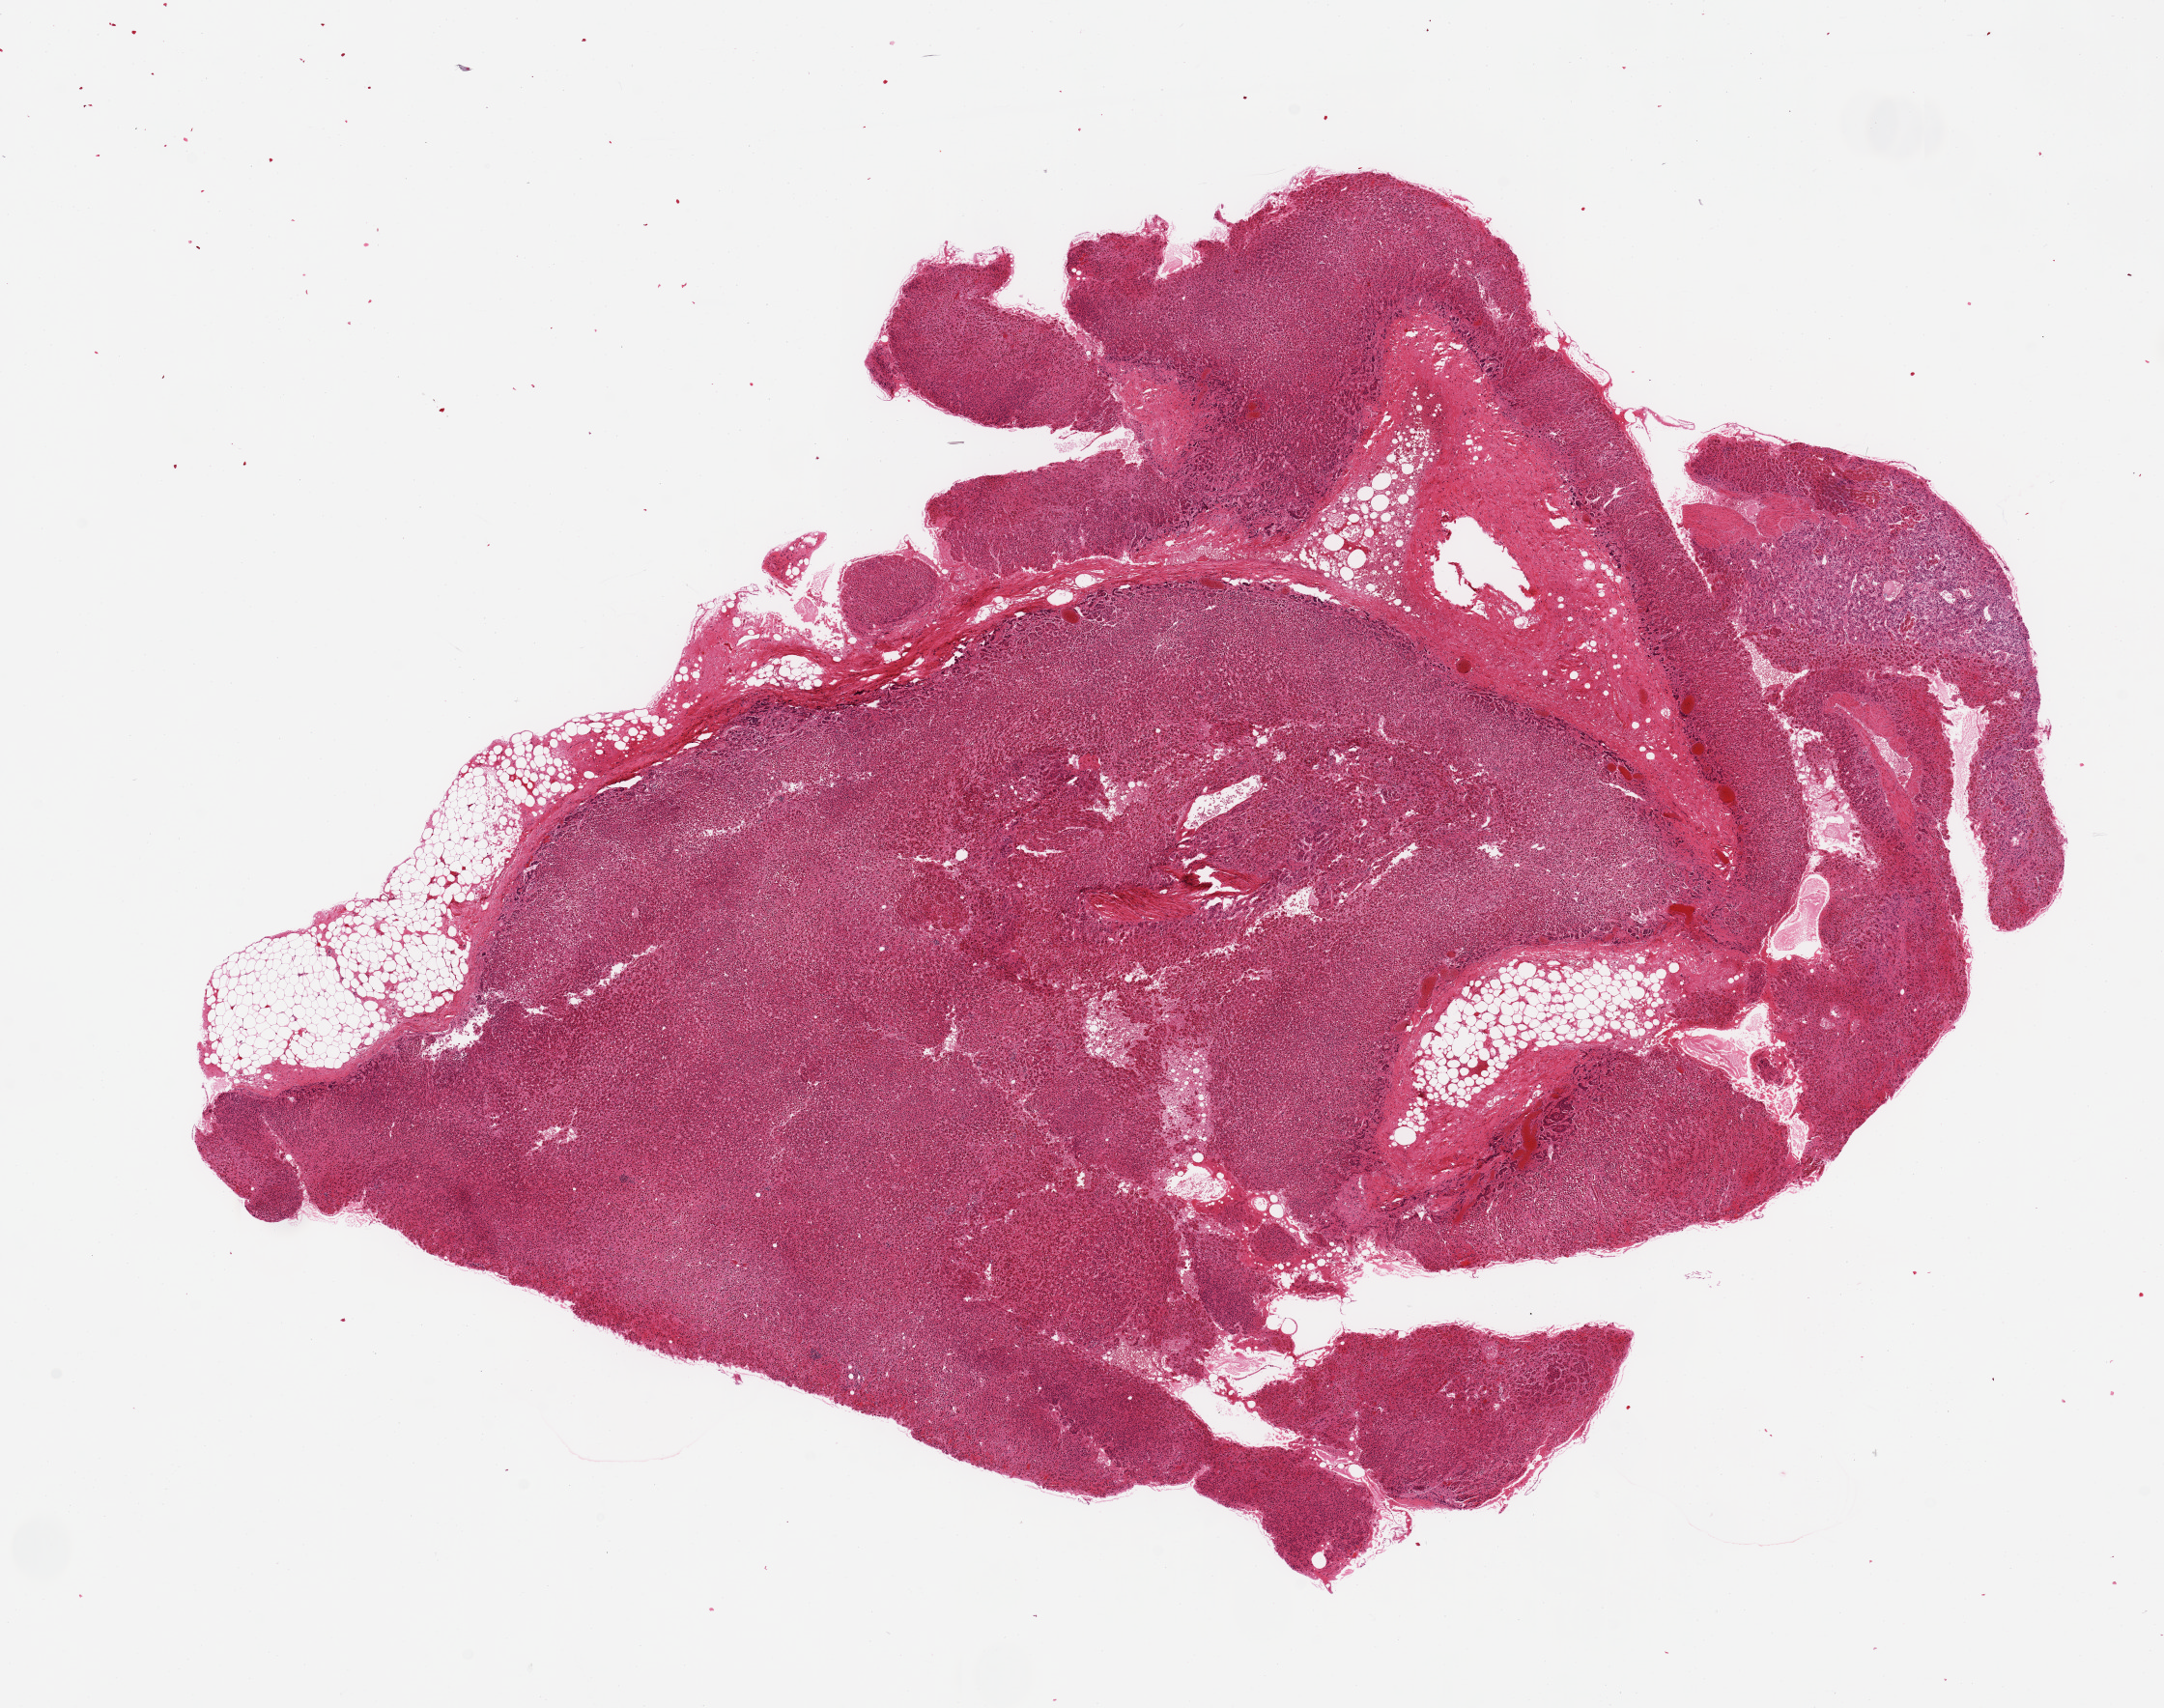
Whole-slide image, hematoxylin and eosin (H&E) stain, a low-resolution overview of the entire scanned area, about 17.7 x 14.0 mm. PAXgene-fixed, paraffin-embedded tissue. Section of adrenal gland (target tissue). Tissue donor sample. Donor sex: male.
• pathologist's review note for this sample: 90% of specimen is cortex, moderate autolysis